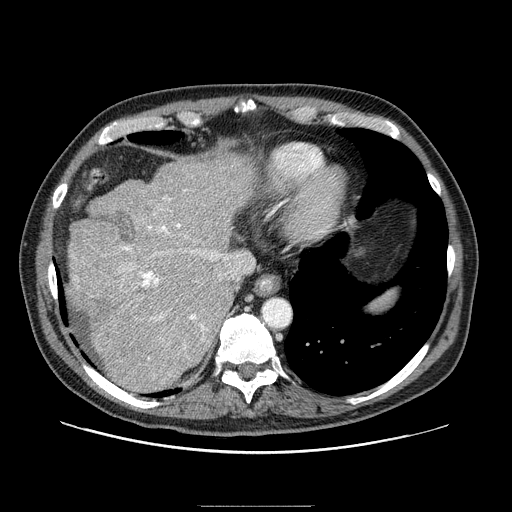
Contrast-enhanced abdominal CT (liver protocol), one axial slice; slice 70 of 99 in the series (ordered by position); one of 2 acquisitions stored at this slice position; soft-tissue window (W 400 / L 40 HU); 512 × 512 image matrix, field of view 400 × 400 mm. Case-level facts recorded for this patient, not image findings: diagnosis: hepatocellular carcinoma (patient treated with transarterial chemoembolisation; whether this scan precedes or follows treatment is not stated here); TNM stage (as recorded): Stage-II; Child-Pugh class: A; tumour differentiation: well differentiated; tumour nodularity: multinodular.
Annotated regions visible in this slice (semi-automatic segmentation, software-assisted and operator-edited):
- abdominal aorta: bounding box [x1, y1, x2, y2] px = [263, 298, 291, 327]
- liver parenchyma outside the tumour (the mass and vessels are separate outlines, so this box may not span the whole liver): [66, 154, 254, 390]
- liver vessels: [121, 190, 226, 359]